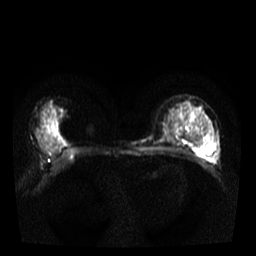
Breast MRI, one axial slice; slice 23 of 40 in the series (ordered by position); diffusion-weighted series; image 2 of 4 stored at this slice position (different b-values; order by instance number); 3 T; 5 mm slice thickness; 256 × 256 image matrix, field of view 320 × 320 mm. Female patient.
Structures marked on this image (outlined manually by an expert reader):
- tumour on diffusion-weighted imaging: bounding box [x1, y1, x2, y2] px = [199, 143, 211, 149]